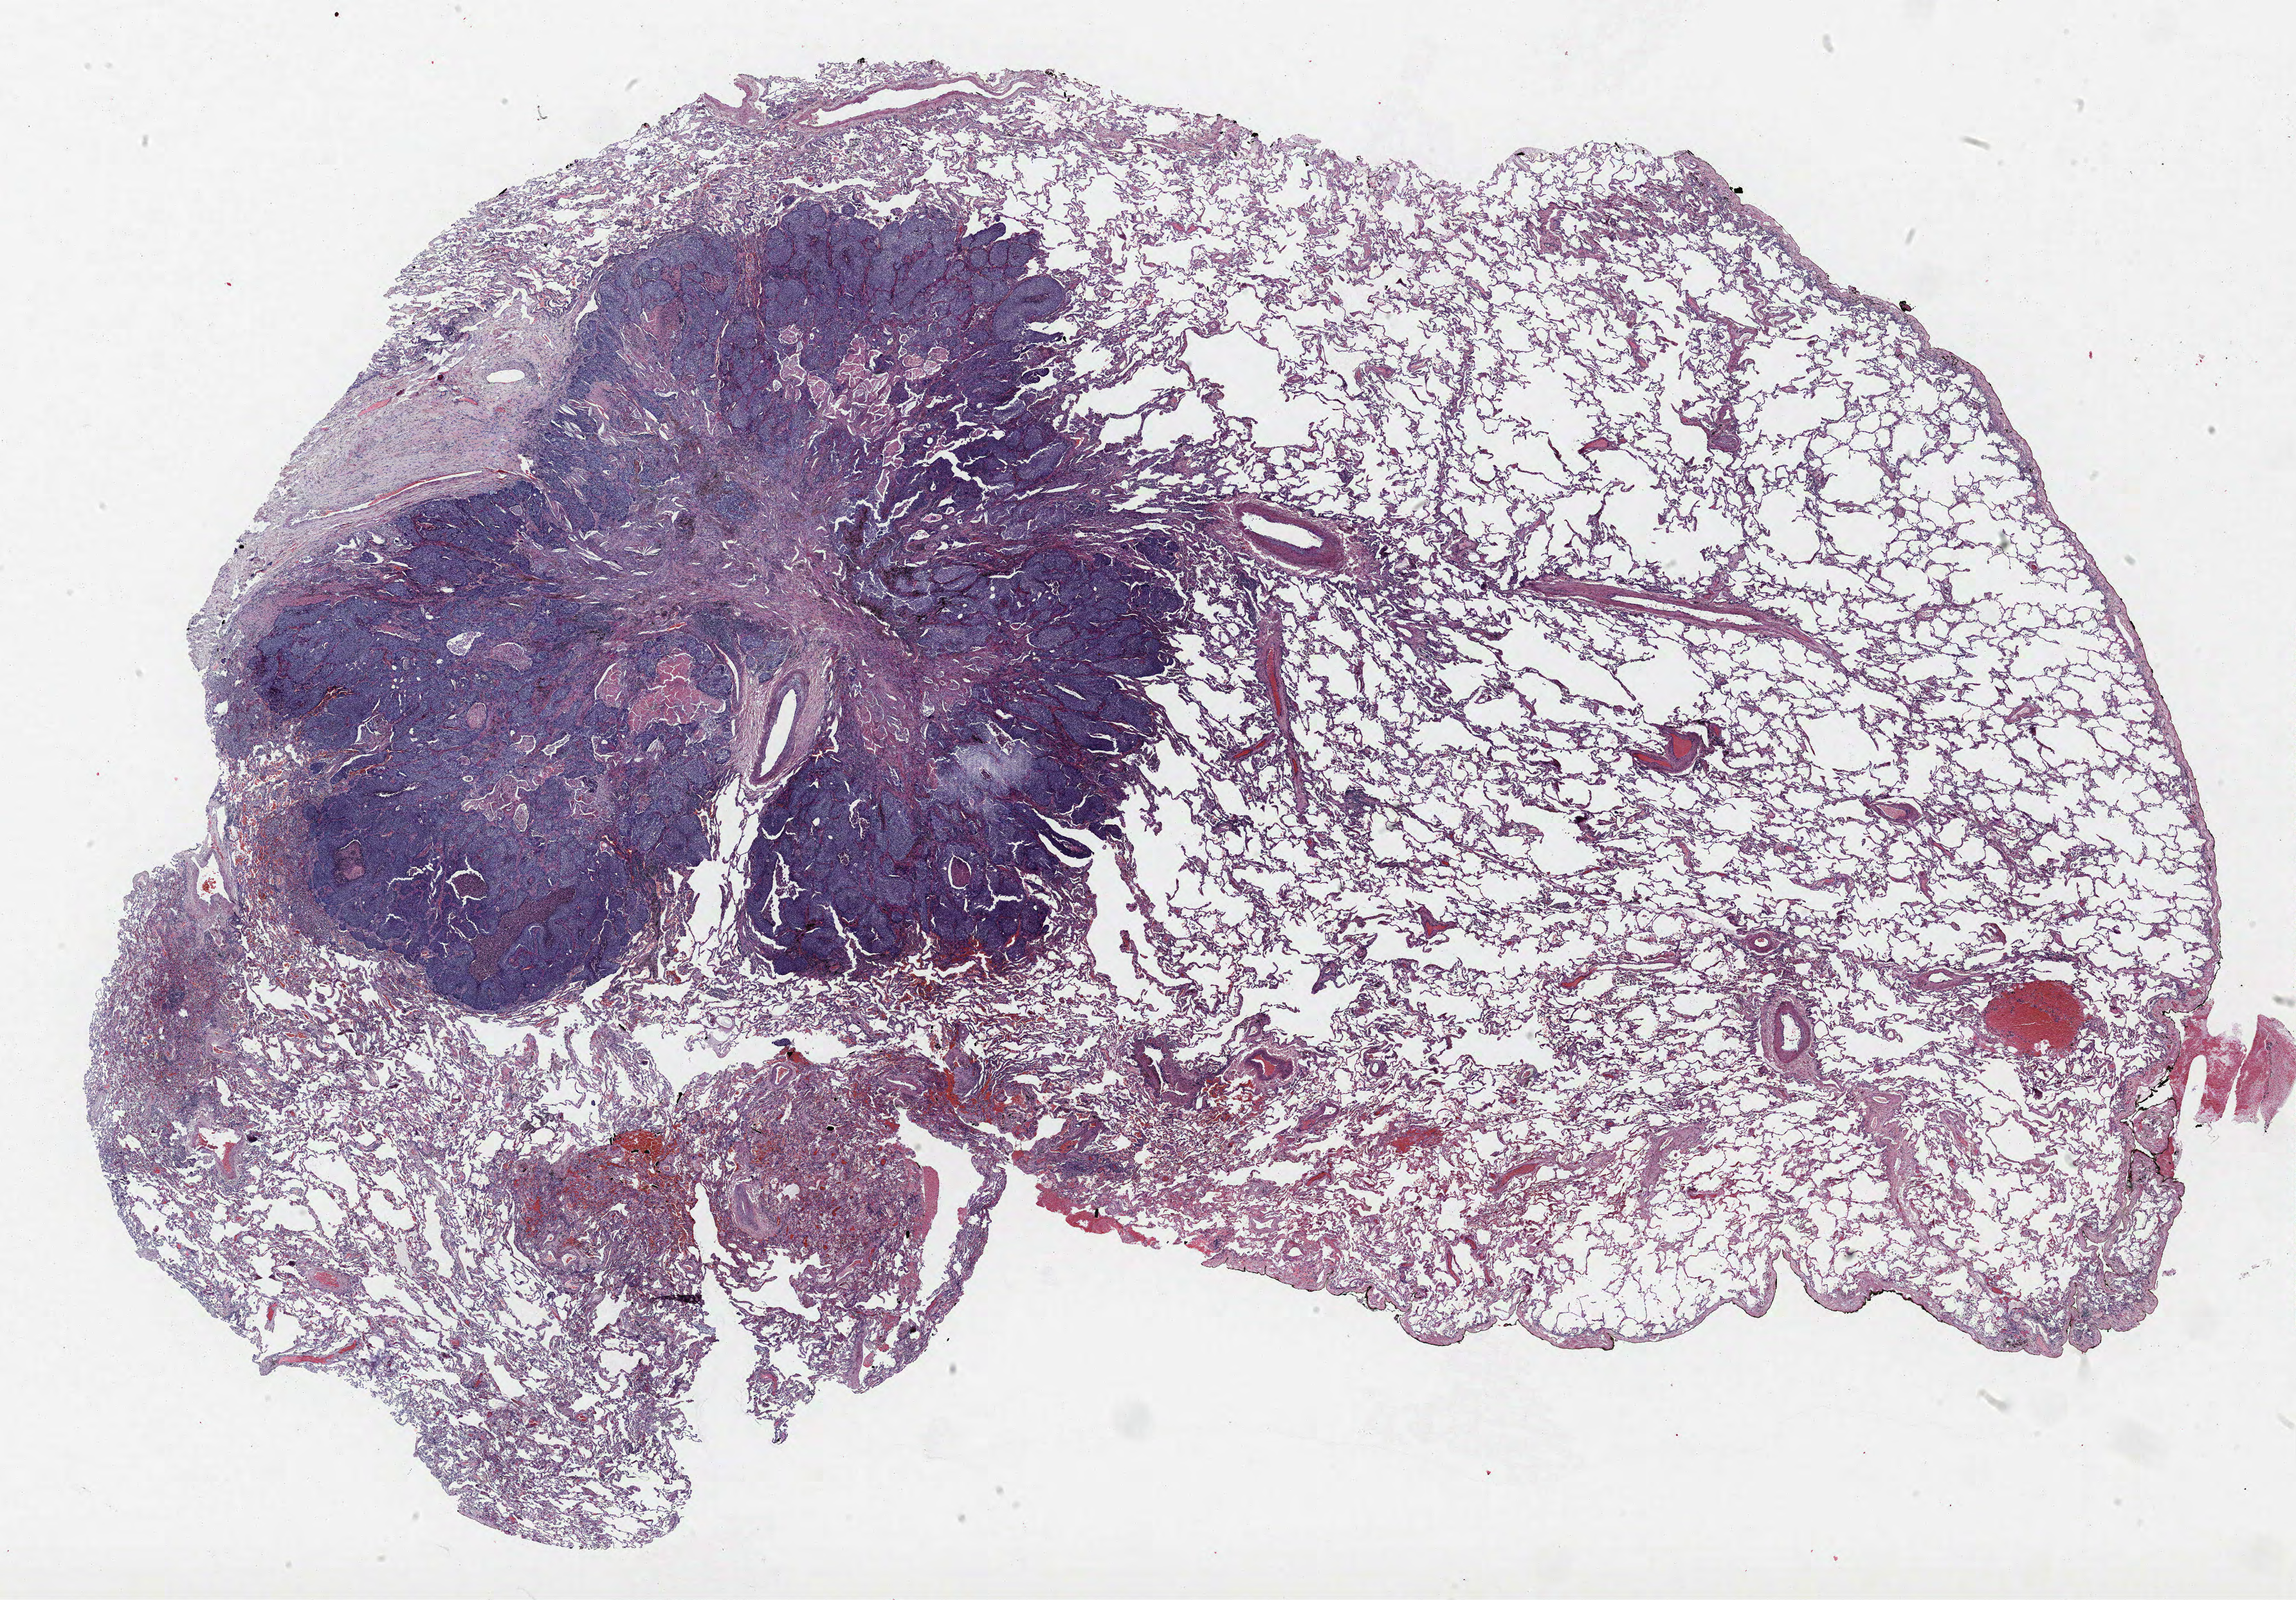
H&E-stained whole-slide image — shown as a low-resolution overview of the whole scanned area (about 28.6 x 19.9 mm, acquisition: 40x scan); formalin-fixed paraffin-embedded (FFPE) section; lung tissue. Male patient, aged 69 at enrolment. Former smoker at enrolment.
Participant's lung-cancer diagnosis: Squamous cell carcinoma, NOS.